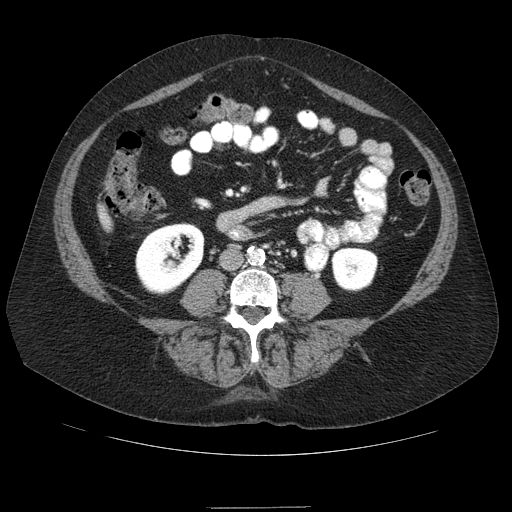
Contrast-enhanced abdominal CT (liver protocol), one axial slice. Position 9 of 89 along the scan axis. Reconstruction kernel STANDARD. 120 kVp. Soft-tissue window (W 400 / L 40 HU). 2.5 mm slice thickness. 512 × 512 image matrix. From the clinical record (not read from this slice): diagnosis: hepatocellular carcinoma (patient treated with transarterial chemoembolisation; whether this scan precedes or follows treatment is not stated here); TNM stage (as recorded): Stage-IIIB; Child-Pugh class: A.
Annotated regions visible in this slice (semi-automatically segmented with operator editing):
- liver parenchyma outside the tumour (the mass and vessels are separate outlines, so this box may not span the whole liver): box from (x=98, y=205) to (x=112, y=230) px